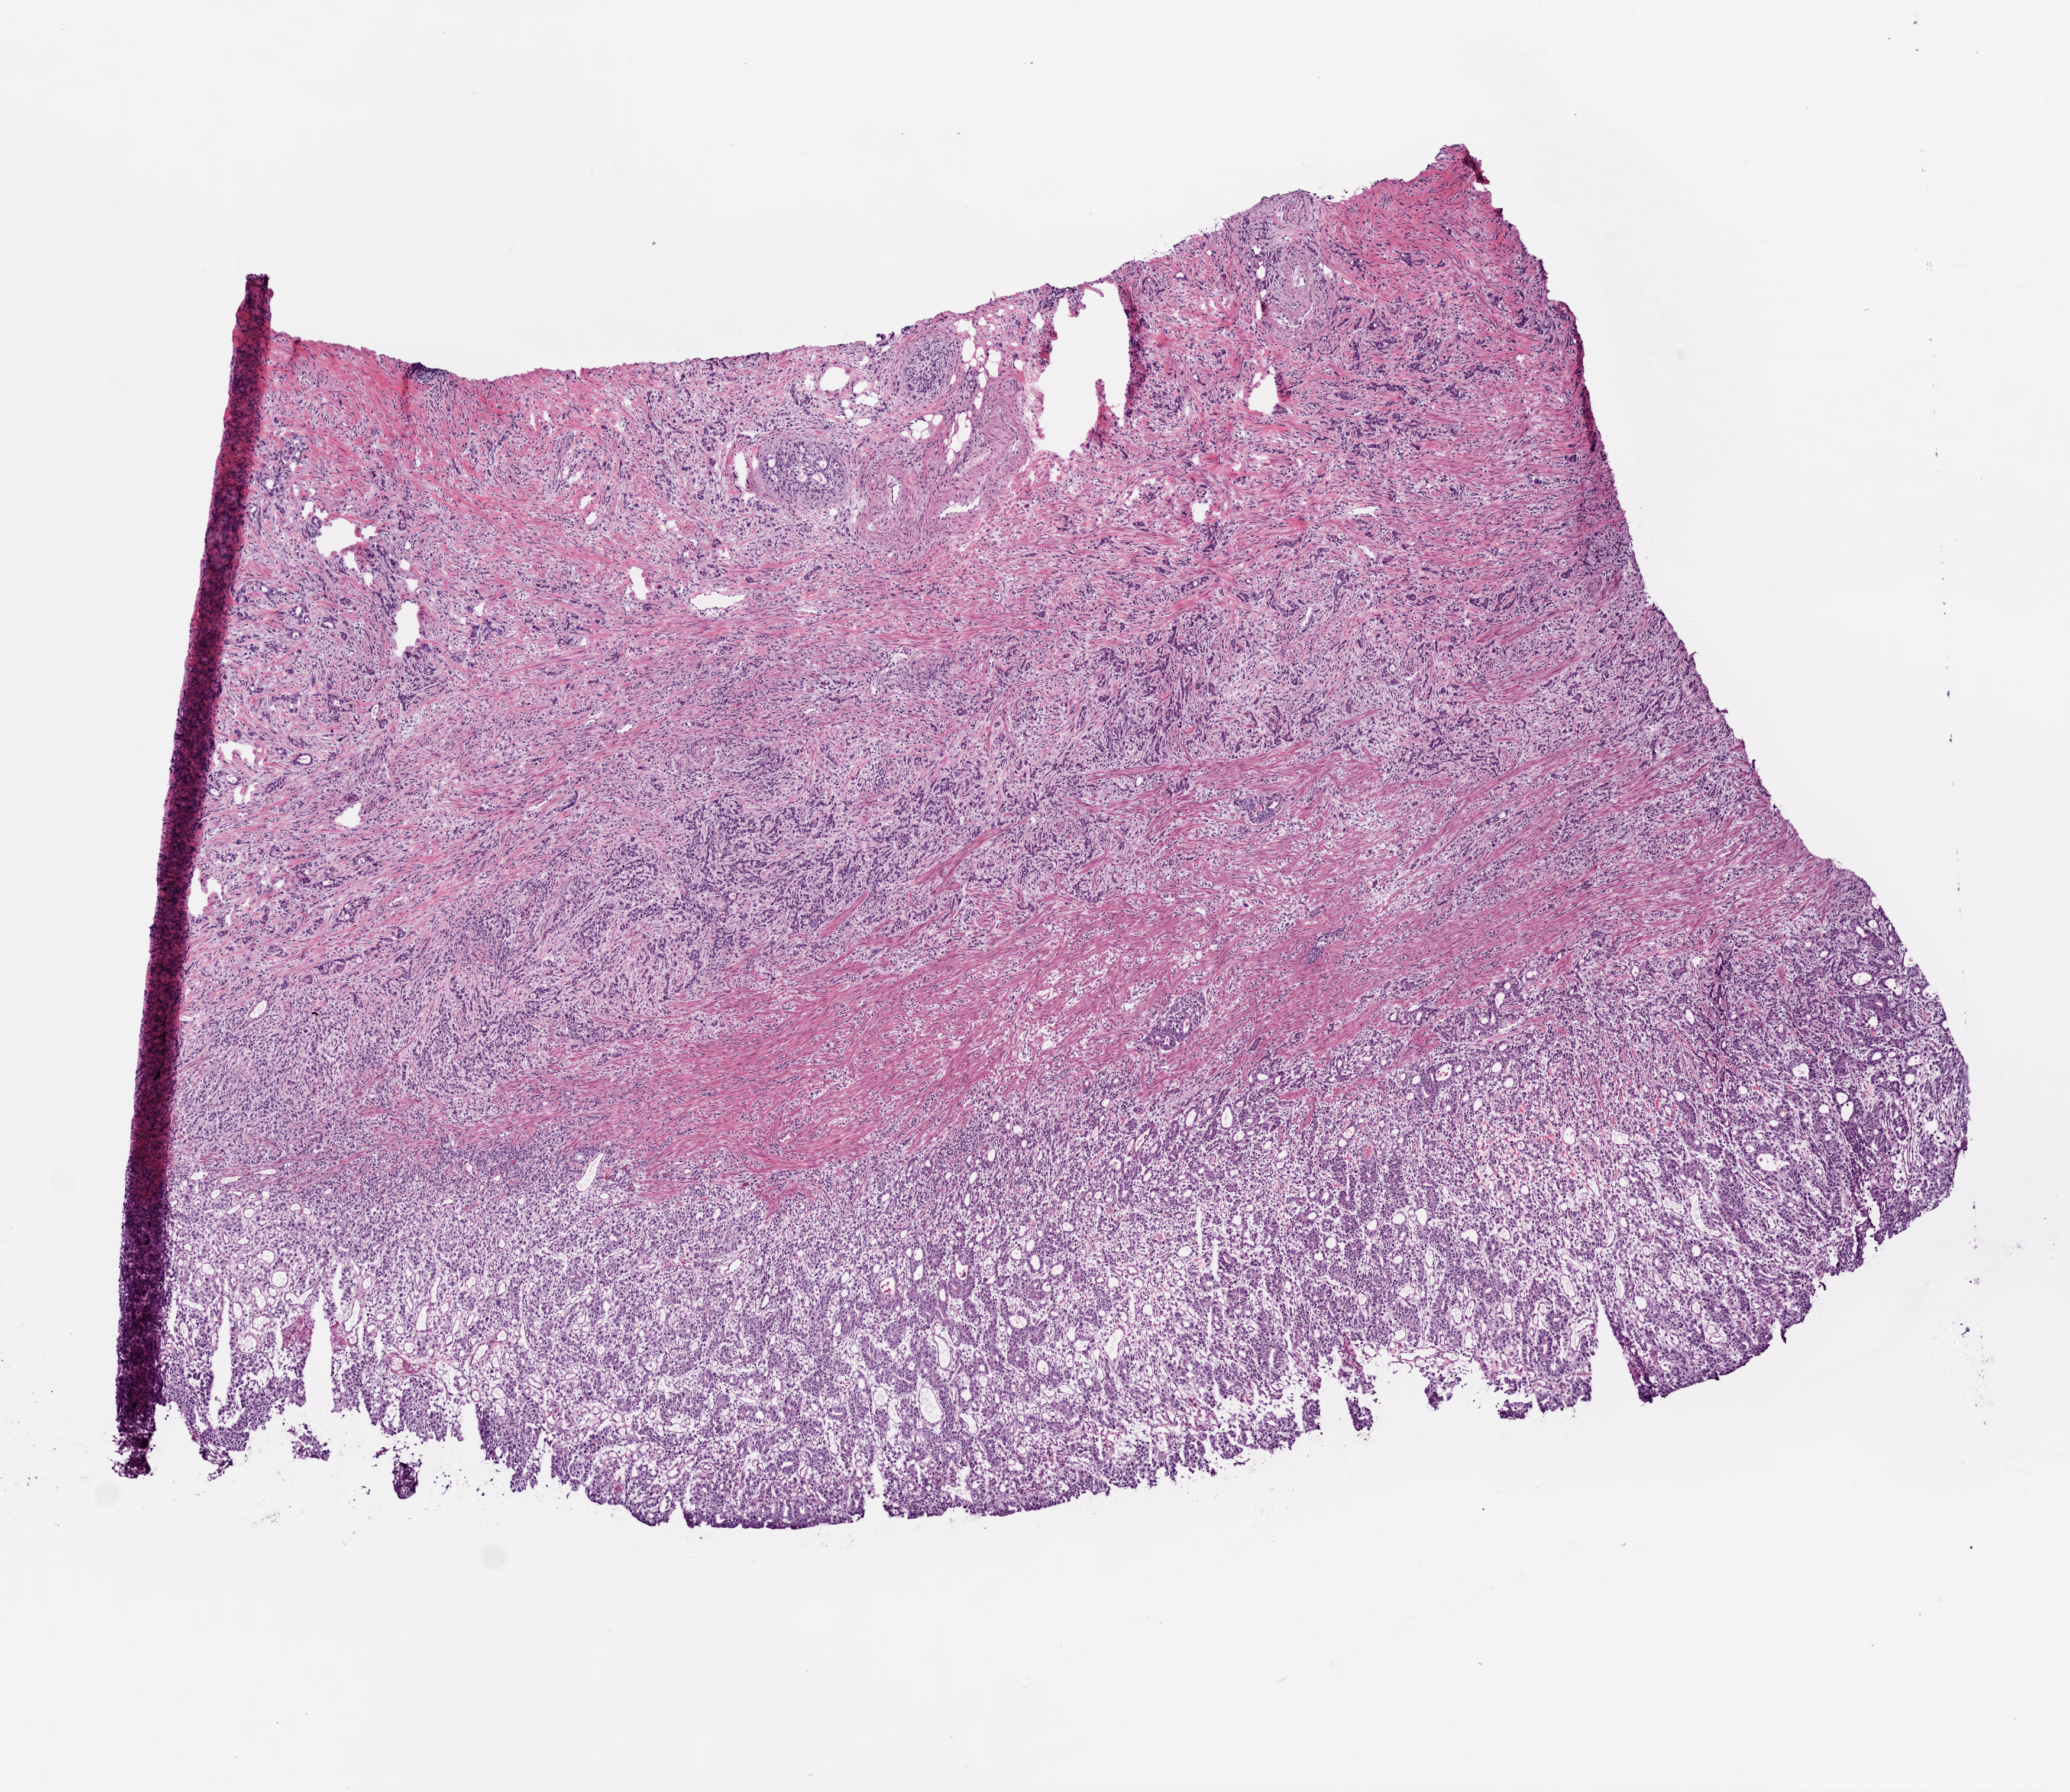
Whole-slide histology image, Hematoxylin and eosin (H&E) stained, a low-resolution overview of the entire scanned area, about 7.0 x 6.1 mm (from a 20x scan); frozen section; sample: primary tumour, stomach. Patient: male, age at initial diagnosis 80 years. Histologic grade: G3 (poorly differentiated). Pathologist review of this section (percent, as recorded): tumour cells 75%, tumour nuclei 80%, normal cells 0%, stromal cells 25%, necrosis 0%.
Histologic diagnosis: Tubular adenocarcinoma (body of stomach). Lymph nodes positive (case pathology): 6 of 19 examined. AJCC pathologic stage: IIIA.